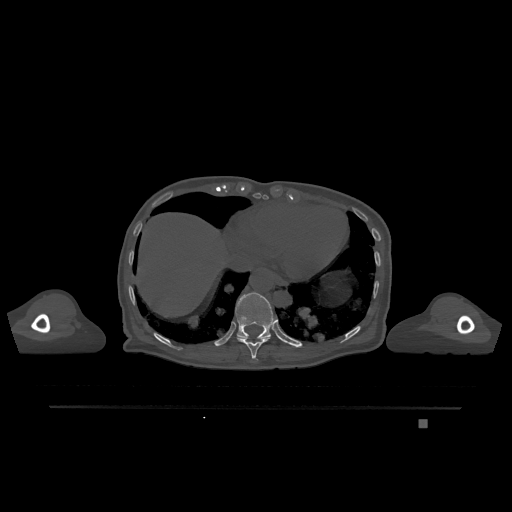
CT including the spine, one axial slice; slice 616 of 1317 in the series (ordered by position); bone window (W 1800 / L 400 HU); 0.5 mm slice thickness; 512 × 512 image matrix, field of view 500 × 500 mm. Patient: female, 74 years. From the clinical record (not read from this slice): primary cancer: lung.
Structures marked on this image (semi-automatically segmented with operator editing):
- T10 vertebra: box from (x=237, y=337) to (x=270, y=359) px
- T11 vertebra: (x=235, y=292)–(x=276, y=339)